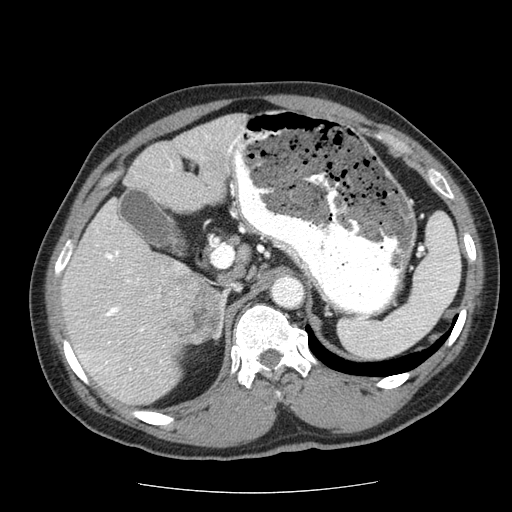
Contrast-enhanced abdominal CT (liver protocol), one axial slice; 120 kVp; soft-tissue window (W 400 / L 40 HU); 2.5 mm slice thickness; 512 × 512 image matrix. From the clinical record (not read from this slice): diagnosis: hepatocellular carcinoma (patient treated with transarterial chemoembolisation; whether this scan precedes or follows treatment is not stated here); TNM stage (as recorded): Stage-IIIA; Child-Pugh class: A; tumour size: 8 cm.
Annotated regions visible in this slice (semi-automatic segmentation, software-assisted and operator-edited):
- abdominal aorta: box from (x=273, y=277) to (x=302, y=305) px
- liver parenchyma outside the tumour (the mass and vessels are separate outlines, so this box may not span the whole liver): (x=60, y=114)–(x=246, y=404)
- mass: (x=160, y=272)–(x=224, y=343)
- liver vessels: (x=79, y=136)–(x=240, y=371)